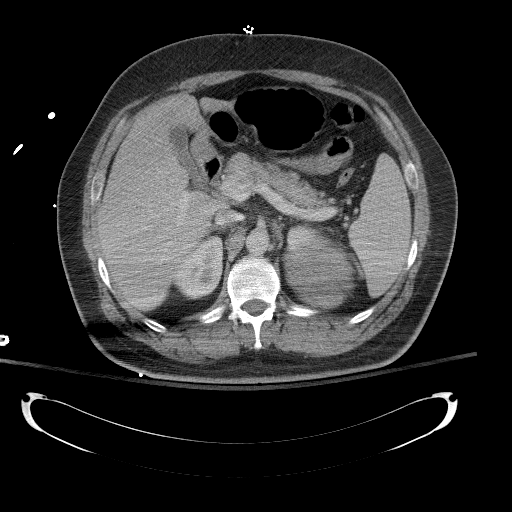
Contrast-enhanced abdominal CT, one axial slice; slice 87 of 154 in the series (ordered by position); 120 kVp; intravenous contrast given; soft-tissue window (W 400 / L 40 HU); 5 mm slice thickness; 512 × 512 image matrix. Male patient, age 43 years. From the clinical record (not read from this slice): diagnosis: adrenocortical carcinoma; tumour side: left adrenal; tumour size at pathology: 9.8 cm; Ki-67 index: 30 %; stage (as recorded): 2.
Structures marked on this image (semi-automatic segmentation, software-assisted and operator-edited):
- mass: box from (x=285, y=239) to (x=351, y=307) px